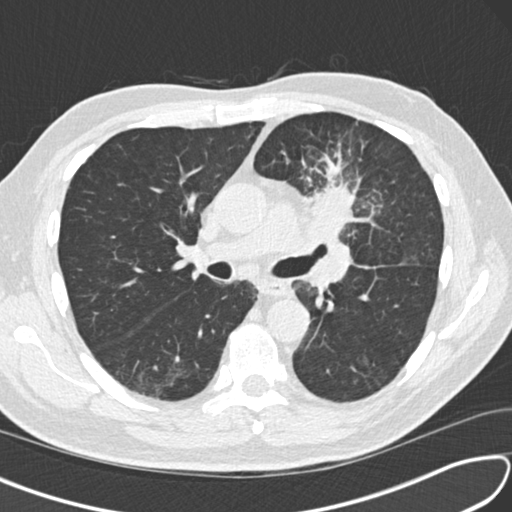
Low-dose screening chest CT, one axial slice; slice 92 of 156 in the series (ordered by position); reconstruction kernel B30f; lung window (W 1500 / L -600 HU); 512 × 512 image matrix, field of view 340 × 340 mm.
Structures marked on this image (outlined manually by an expert reader):
- lesion 1 (tumor, upper lobe of left lung): bounding box [x1, y1, x2, y2] px = [305, 184, 354, 243]